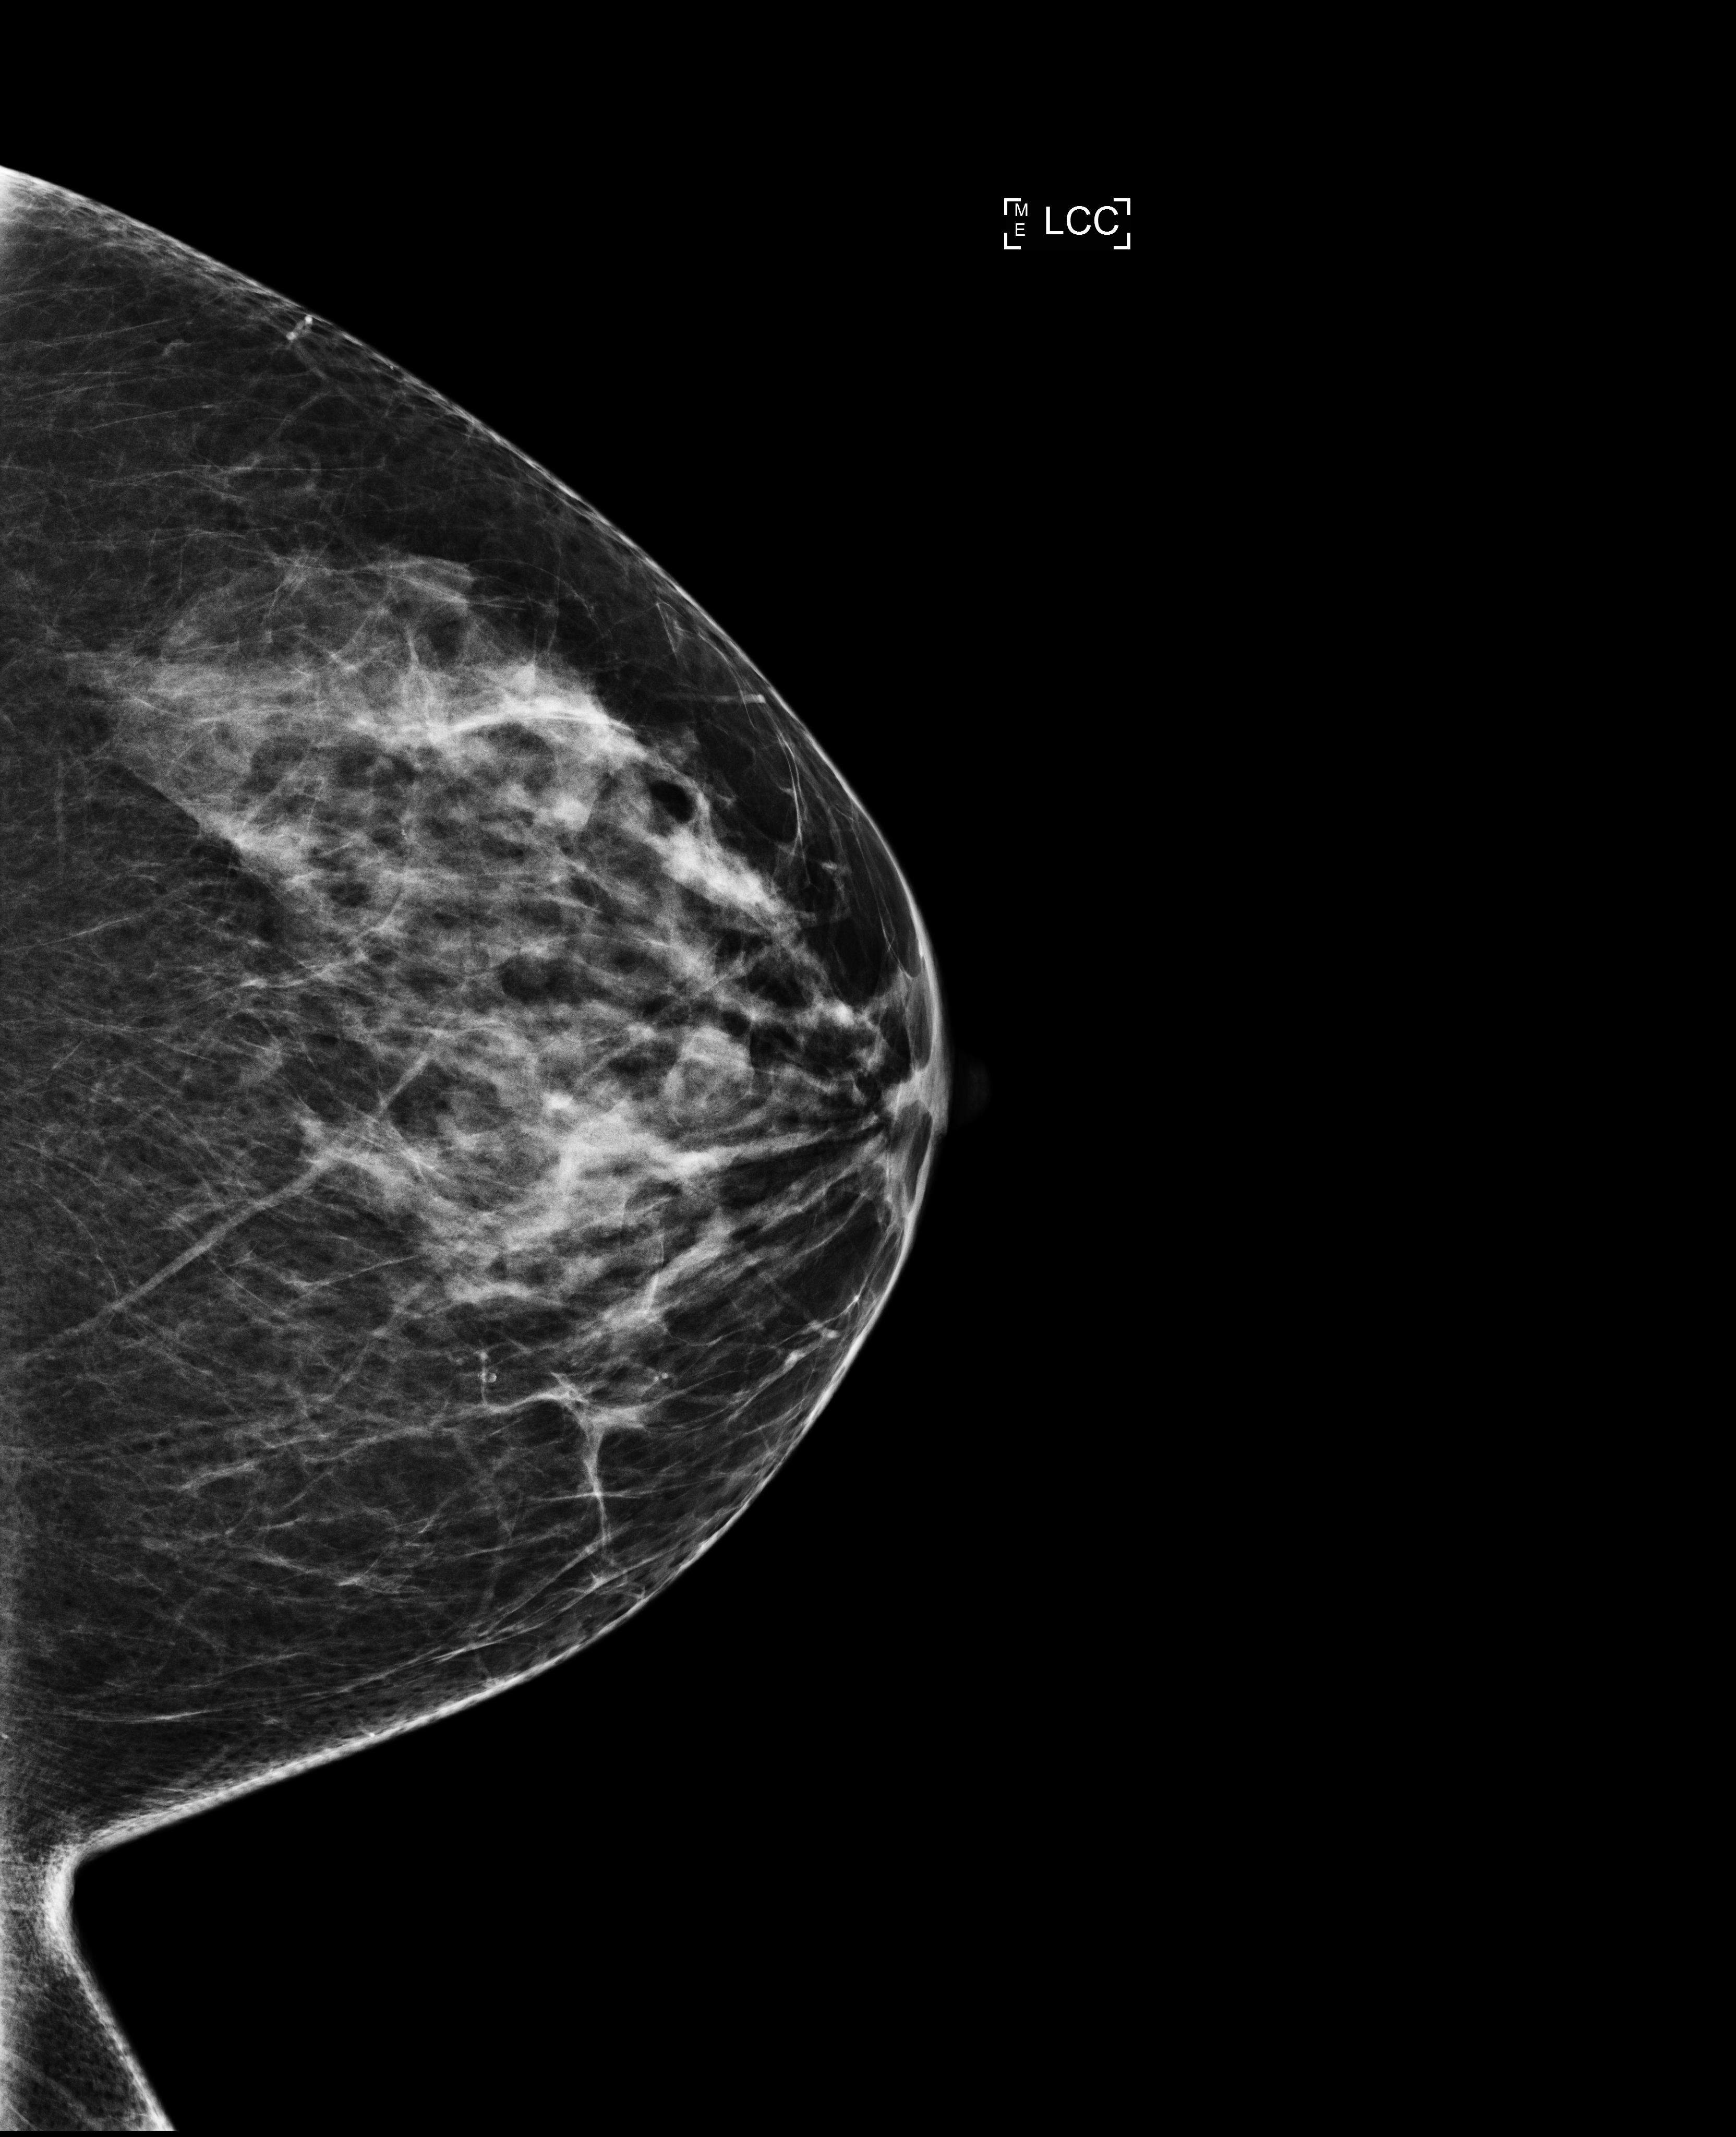
Screening examination; compressed breast thickness 59 mm. Female patient, age 52 years.
Image type: full-field digital mammogram. Breast: left. Projection: CC view.